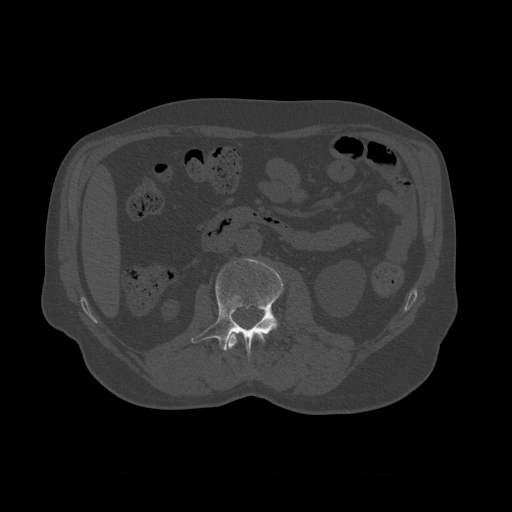
CT including the spine, one axial slice. Slice 330 of 450 in the series (ordered by position). Reconstruction kernel STANDARD. Bone window (W 1800 / L 400 HU). 1.25 mm slice thickness. 512 × 512 image matrix. Patient age 75 years. From the clinical record (not read from this slice): primary cancer: prostate.
Outlined on this slice (semi-automatic segmentation, software-assisted and operator-edited):
- L1 vertebra: bounding box (x1, y1, x2, y2) in pixels: (226, 332, 266, 351)
- L2 vertebra: (191, 259, 284, 361)